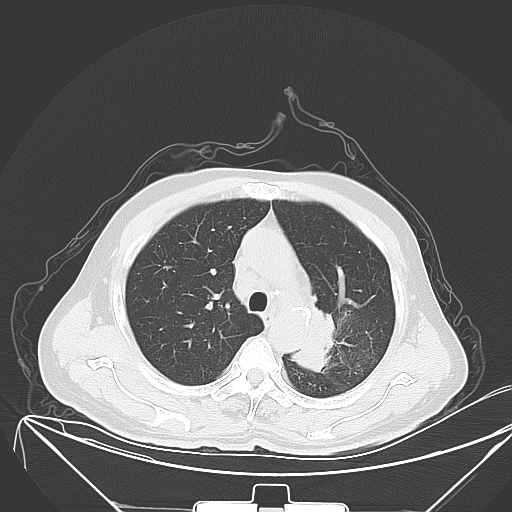
Chest CT, one axial slice; position 43 of 64 along the scan axis; 120 kVp; lung window (W 1500 / L -600 HU); 5 mm slice thickness; 512 × 512 image matrix. Male patient, age 58 years. Case-level facts recorded for this patient, not image findings: clinical TNM (as recorded): T2b N3 M1b.
Annotated regions visible in this slice (bounding box drawn by a radiologist):
- lung tumour (recorded histology: adenocarcinoma): bounding box [x1, y1, x2, y2] px = [290, 305, 338, 378]